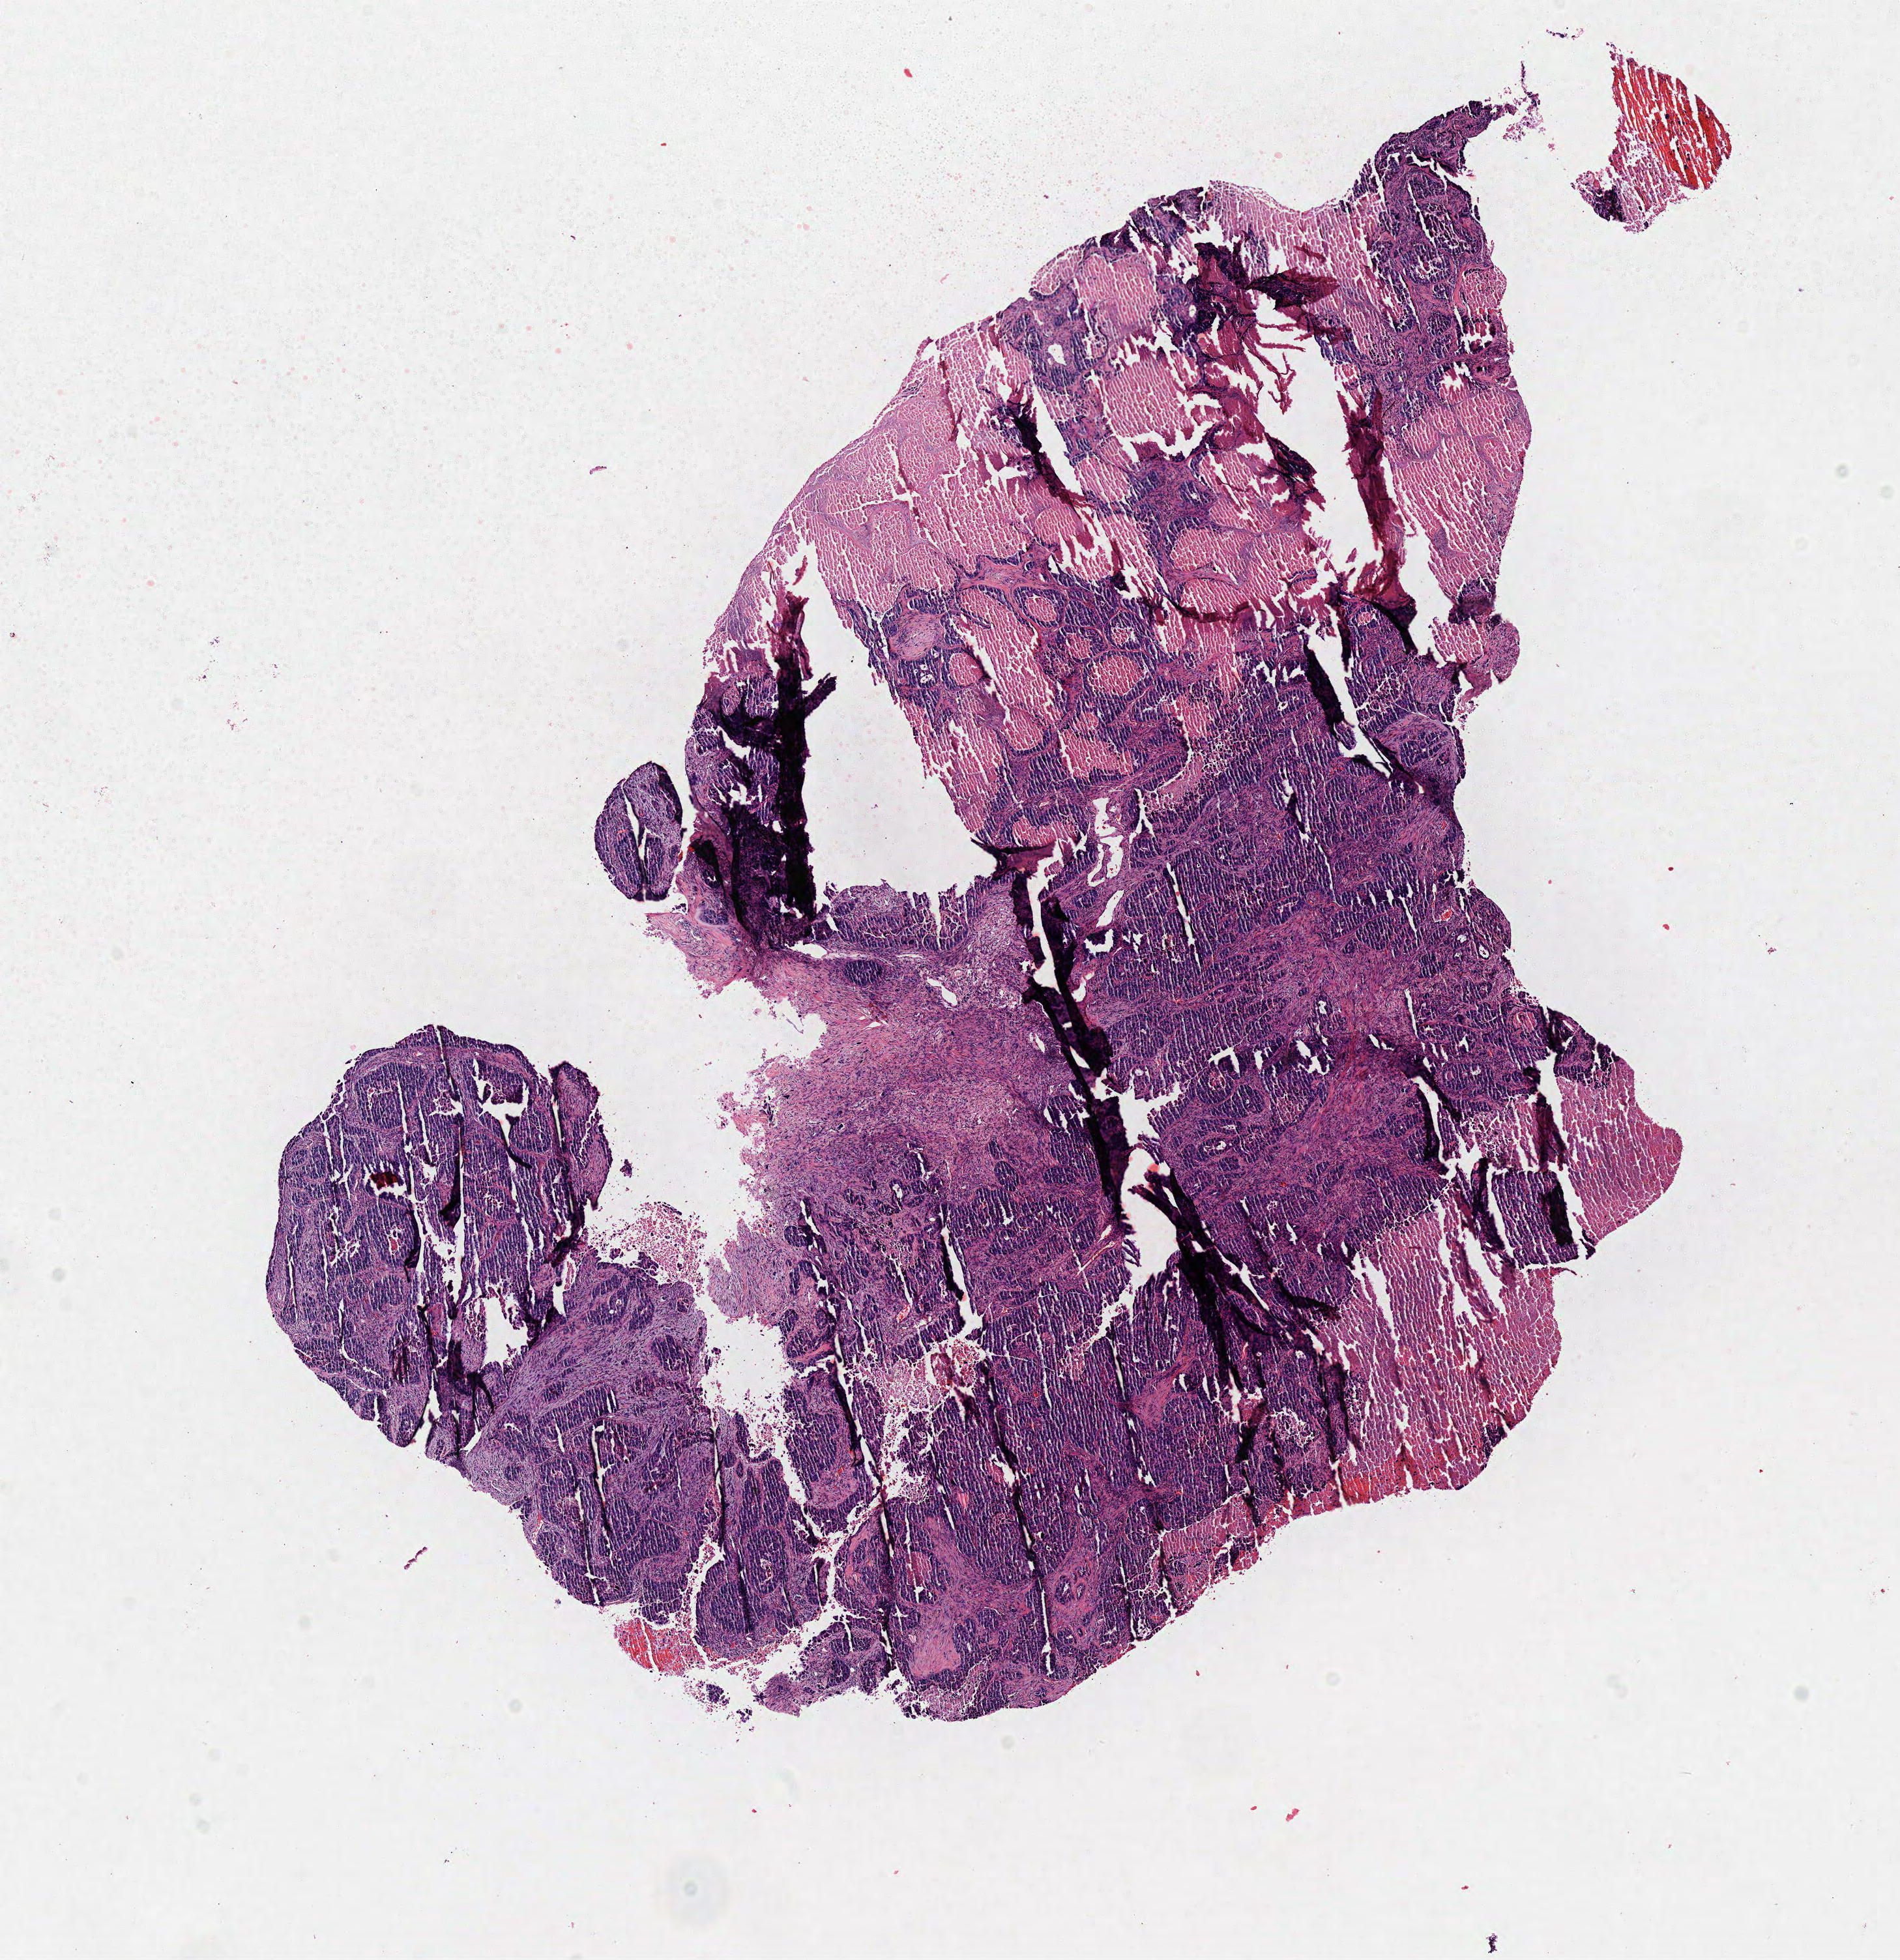
Digitized H&E-stained tissue section (whole slide) — low-resolution overview of the scanned area, about 11.5 x 11.8 mm (slide scanned at 40x). Frozen section from the top of the tissue portion. Primary tumour sample from the lung. Female patient; age at initial diagnosis 62 years. Pathologist review of this section (percent, as recorded): tumour cells 70%, tumour nuclei 65%.
Pathologic diagnosis: Adenocarcinoma, NOS (lower lobe, lung).